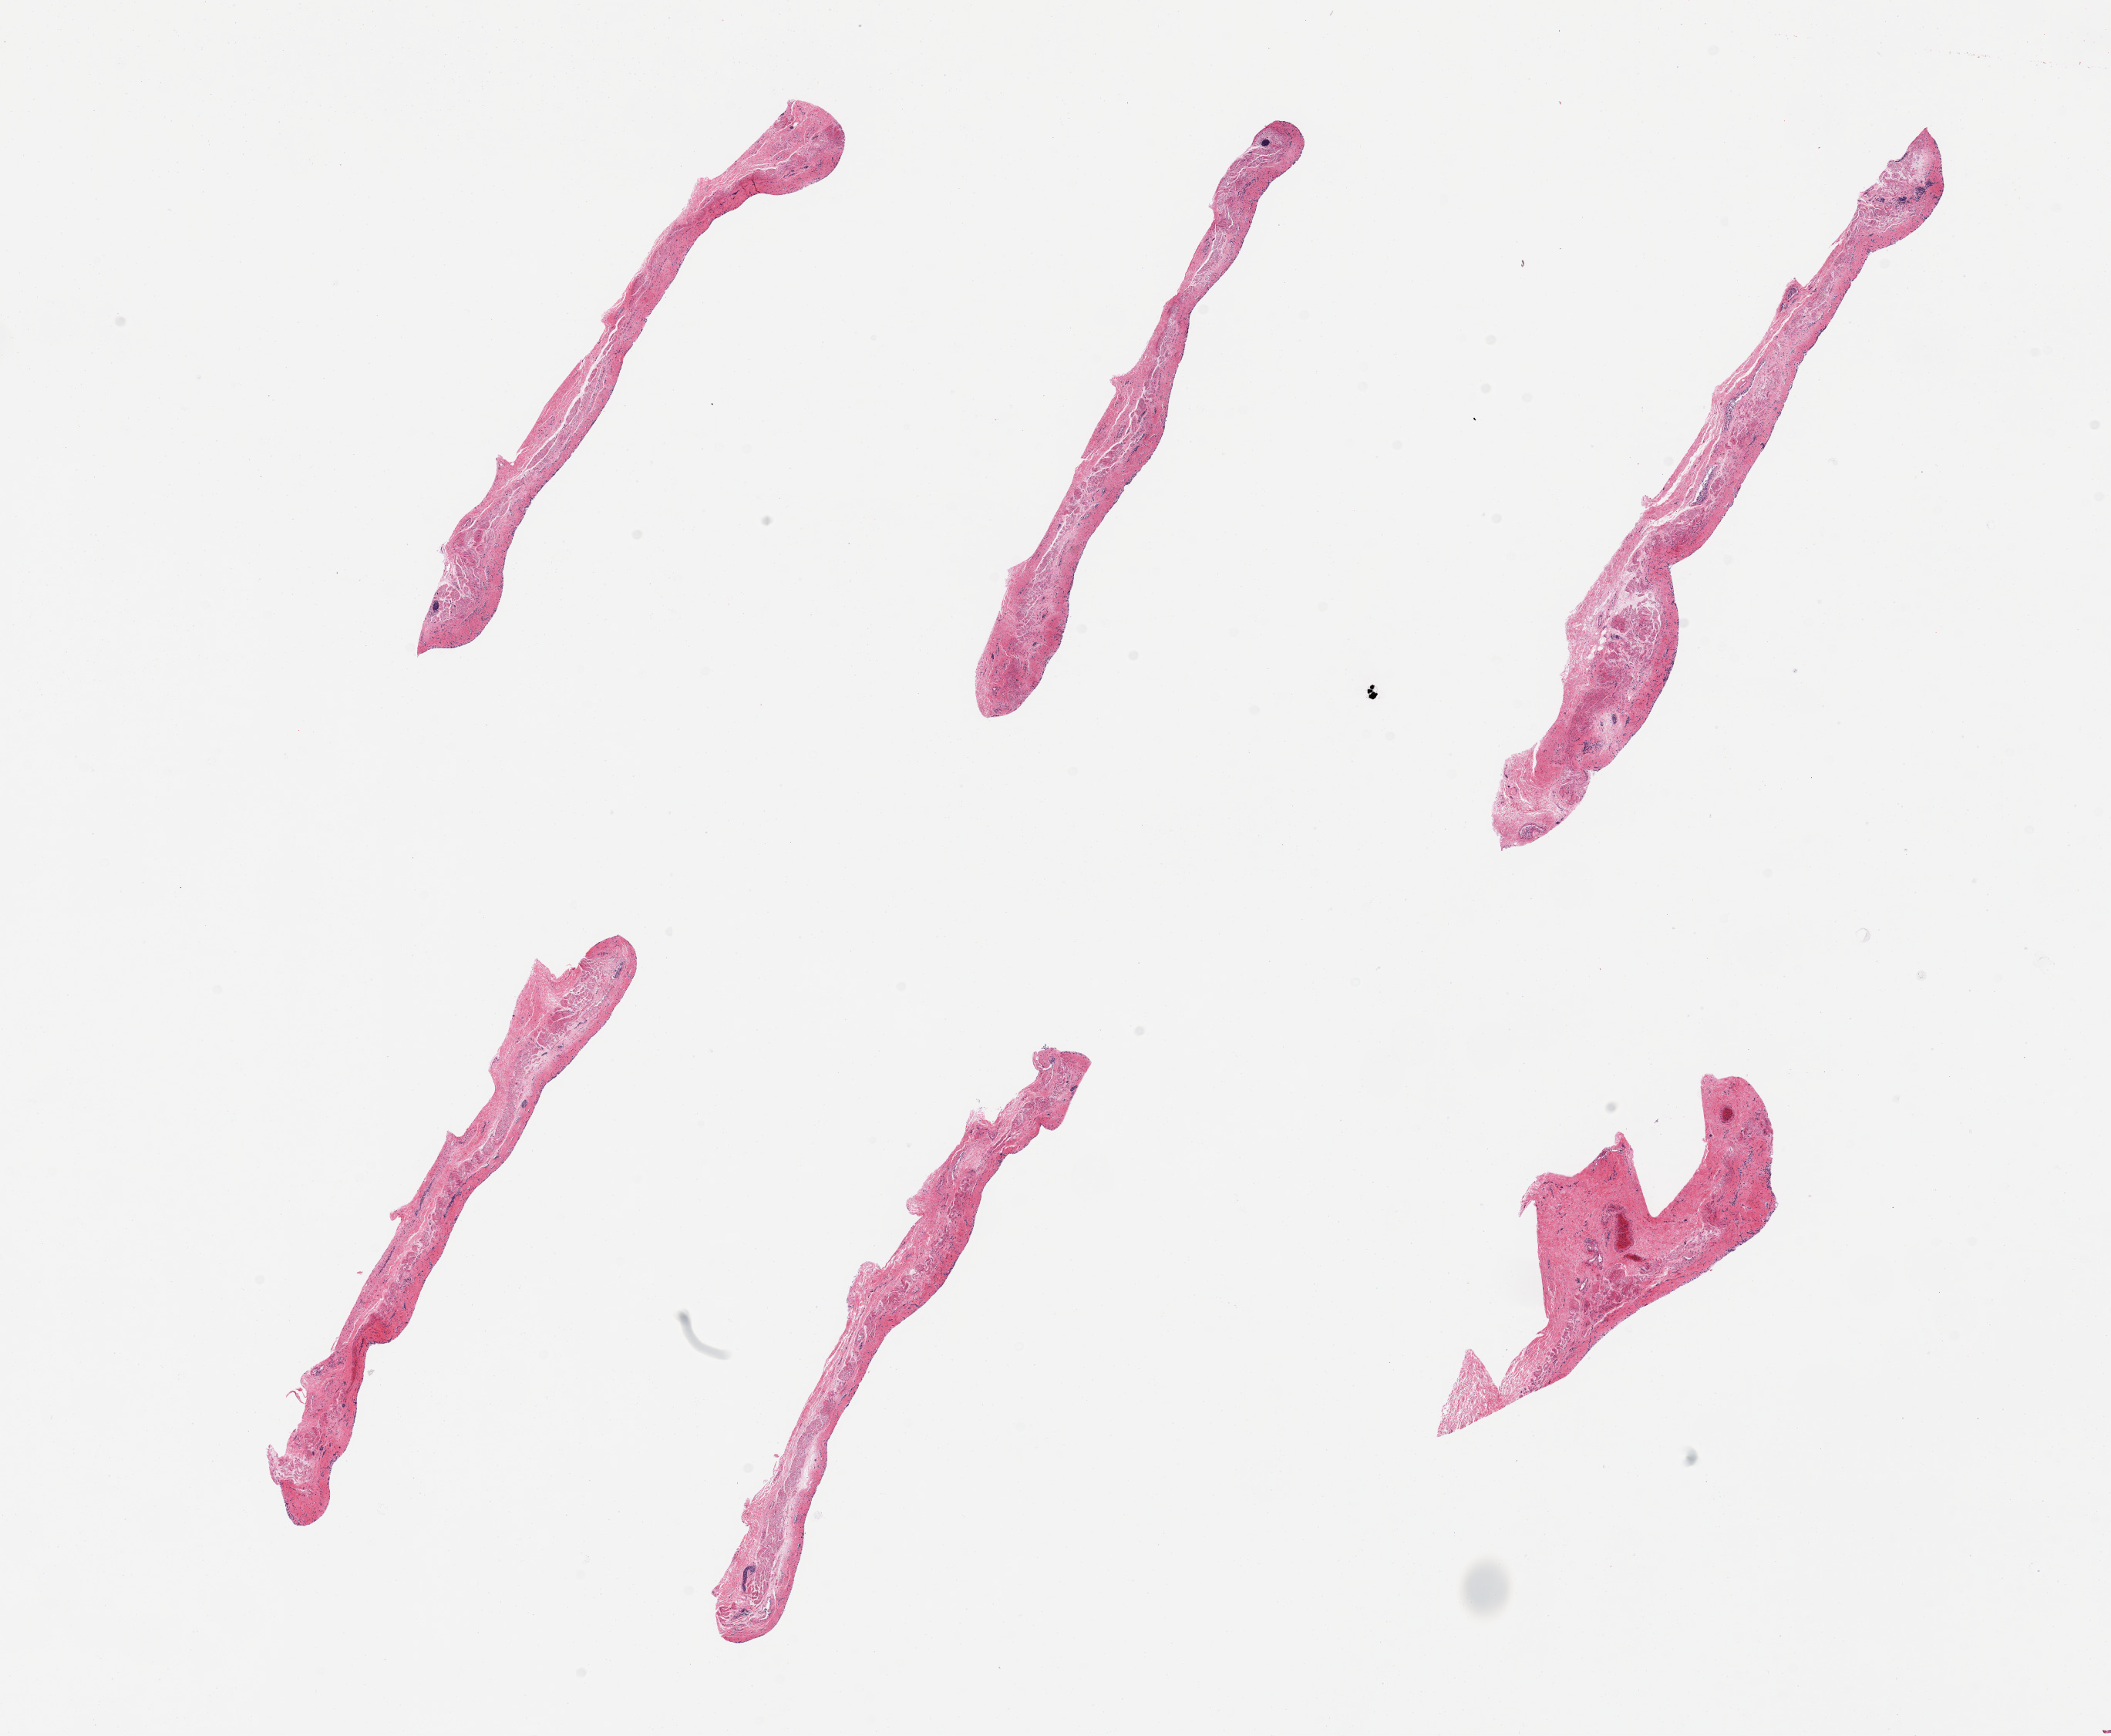
Digitized hematoxylin and eosin (H&E)-stained section, whole scanned area (about 21.7 x 17.8 mm, from a 20x scan) shown as a low-resolution overview. PAXgene-fixed paraffin-embedded (PFPE) section. Sampled site (target tissue): esophageal mucous membrane. Donor tissue sample. Donor sex: male.
Pathologist's review note for this sample: 6 pieces; completely sloughed epithelium.